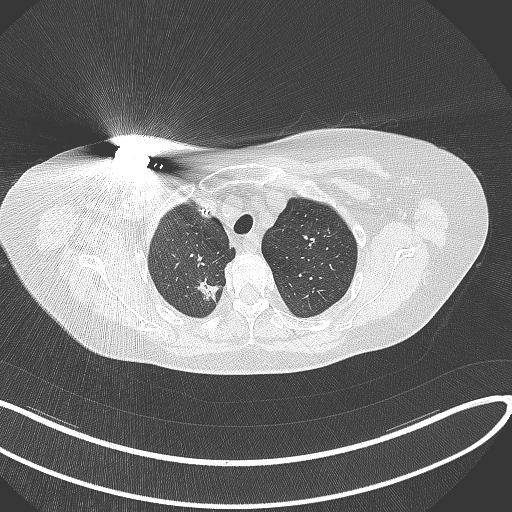
Chest CT, one axial slice. Slice 277 of 316 in the series (ordered by position). Reconstruction kernel B70f. 120 kVp. Lung window (W 1500 / L -600 HU). 1 mm slice thickness. 512 × 512 image matrix, field of view 400 × 400 mm. Female patient, age 72 years. Case-level facts recorded for this patient, not image findings: clinical TNM (as recorded): T1c N0 M0.
Structures marked on this image (bounding box drawn by a radiologist):
- lung tumour (recorded histology: adenocarcinoma): bounding box <194,274,222,303> (left, top, right, bottom; pixels)